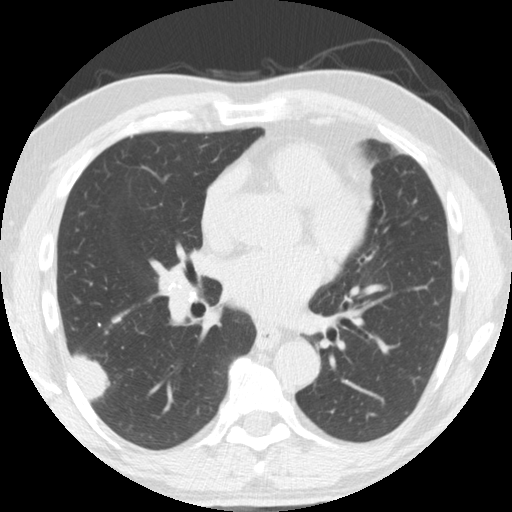
Chest CT (low-dose screening protocol), one axial image; second annual screen; lung window (W 1500 / L -600 HU); 2.5 mm slice thickness. Male participant, aged 61 years at enrolment. Former smoker at enrolment.
• Lesion marked by an expert reader, bounding box (x1, y1, x2, y2) in pixels: (52, 327, 119, 402).
• Reader record for this screening exam (exam-level; its link to the box is not recorded): non-calcified nodule or mass ≥4 mm, right lower lobe, 33 × 19 mm, smooth margins, soft tissue attenuation, pre-existing on the prior screen: yes; interval growth: yes.
• Official screen result: positive, change unspecified: nodule(s) >= 4 mm or enlarging nodule(s), mass(es), or other non-specific abnormalities suspicious for lung cancer.
• Participant outcome: lung cancer diagnosed 30 days after this screen — adenosquamous carcinoma, right lower lobe, poorly differentiated (G3), stage IV (AJCC 6th edition), 45 mm at pathology.